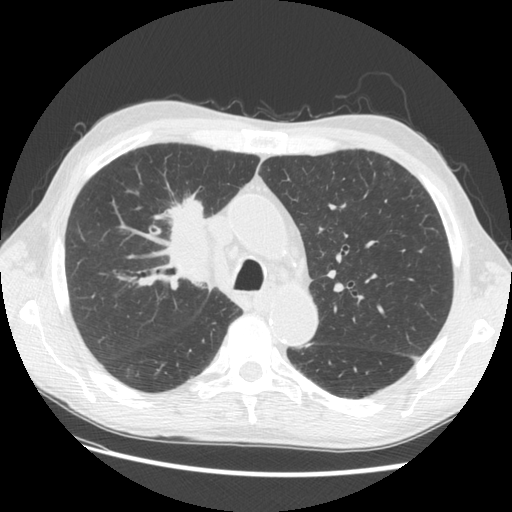
Low-dose screening chest CT, one axial slice; position 92 of 133 along the scan axis; reconstruction kernel STANDARD; 120 kVp; lung window (W 1500 / L -600 HU); 512 × 512 image matrix, field of view 360 × 360 mm.
Structures marked on this image (manually delineated by an expert):
- lesion 1 (tumor, hilum of right lung): bounding box <155,198,210,281> (left, top, right, bottom; pixels)